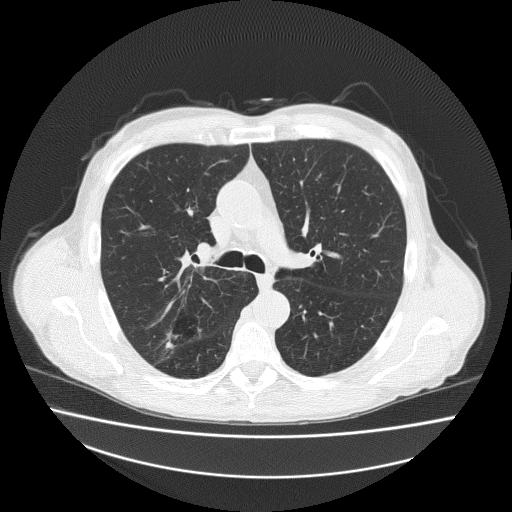
Axial slice from a low-dose chest CT screening exam. Second screening round (one year after baseline). Lung window (W 1500 / L -600 HU). Slice 74 of 186 in the series. 512 × 512 image matrix. Male participant, aged 73 years at enrolment.
• Expert reader's lesion annotation, bounding box <154,311,208,351> (left, top, right, bottom; pixels).
• No non-calcified nodule or mass ≥4 mm was recorded by the screening reader at this exam.
• Official screen result: negative screen, minor abnormalities not suspicious for lung cancer.
• Later outcome: lung cancer diagnosed 418 days after this screen — adenosquamous carcinoma, right upper lobe, well differentiated (G1), stage IA (AJCC 6th edition), 20 mm at pathology.